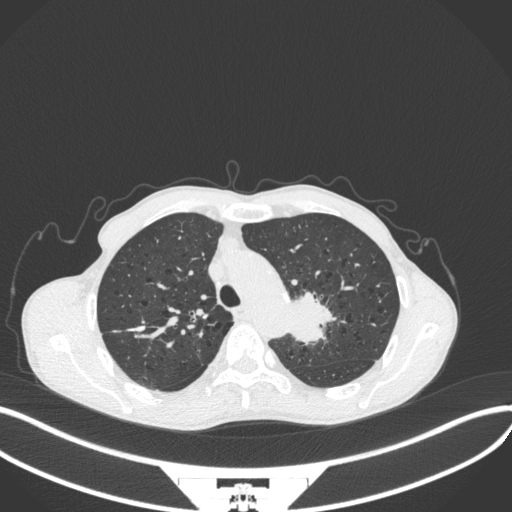
Chest CT, one axial slice; slice 315 of 394 in the series (ordered by position); reconstruction kernel B31f; 120 kVp; lung window (W 1500 / L -600 HU); 1 mm slice thickness; 512 × 512 image matrix. Patient: male, 65 years. From the clinical record (not read from this slice): clinical TNM (as recorded): T2b N0 M0.
Structures marked on this image (bounding box drawn by a radiologist):
- lung tumour (recorded histology: adenocarcinoma): bounding box [x1, y1, x2, y2] px = [284, 286, 345, 350]